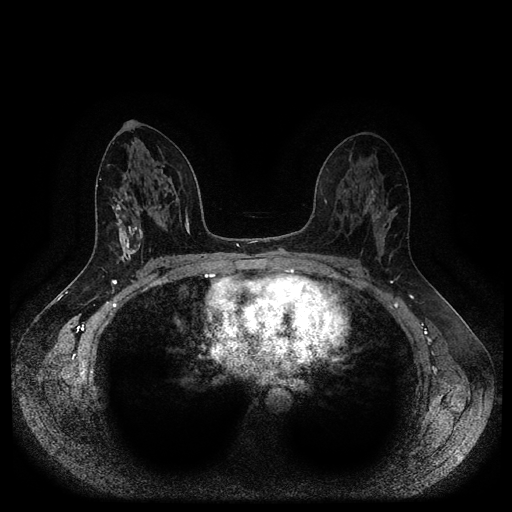
Breast MRI (dynamic contrast-enhanced, multi-phase), one axial slice; dynamic contrast-enhanced series, time point 2 of 5 at this slice position (early post-contrast); 1.5 T; TE 2.6 ms, TR 5.3 ms; 2 mm slice thickness; 512 × 512 image matrix, field of view 360 × 360 mm. Patient: female, 45 years.
Structures marked on this image (semi-automatic segmentation, software-assisted and operator-edited):
- breast lesion (labelled benign in the annotation): bounding box [x1, y1, x2, y2] px = [112, 198, 143, 265]